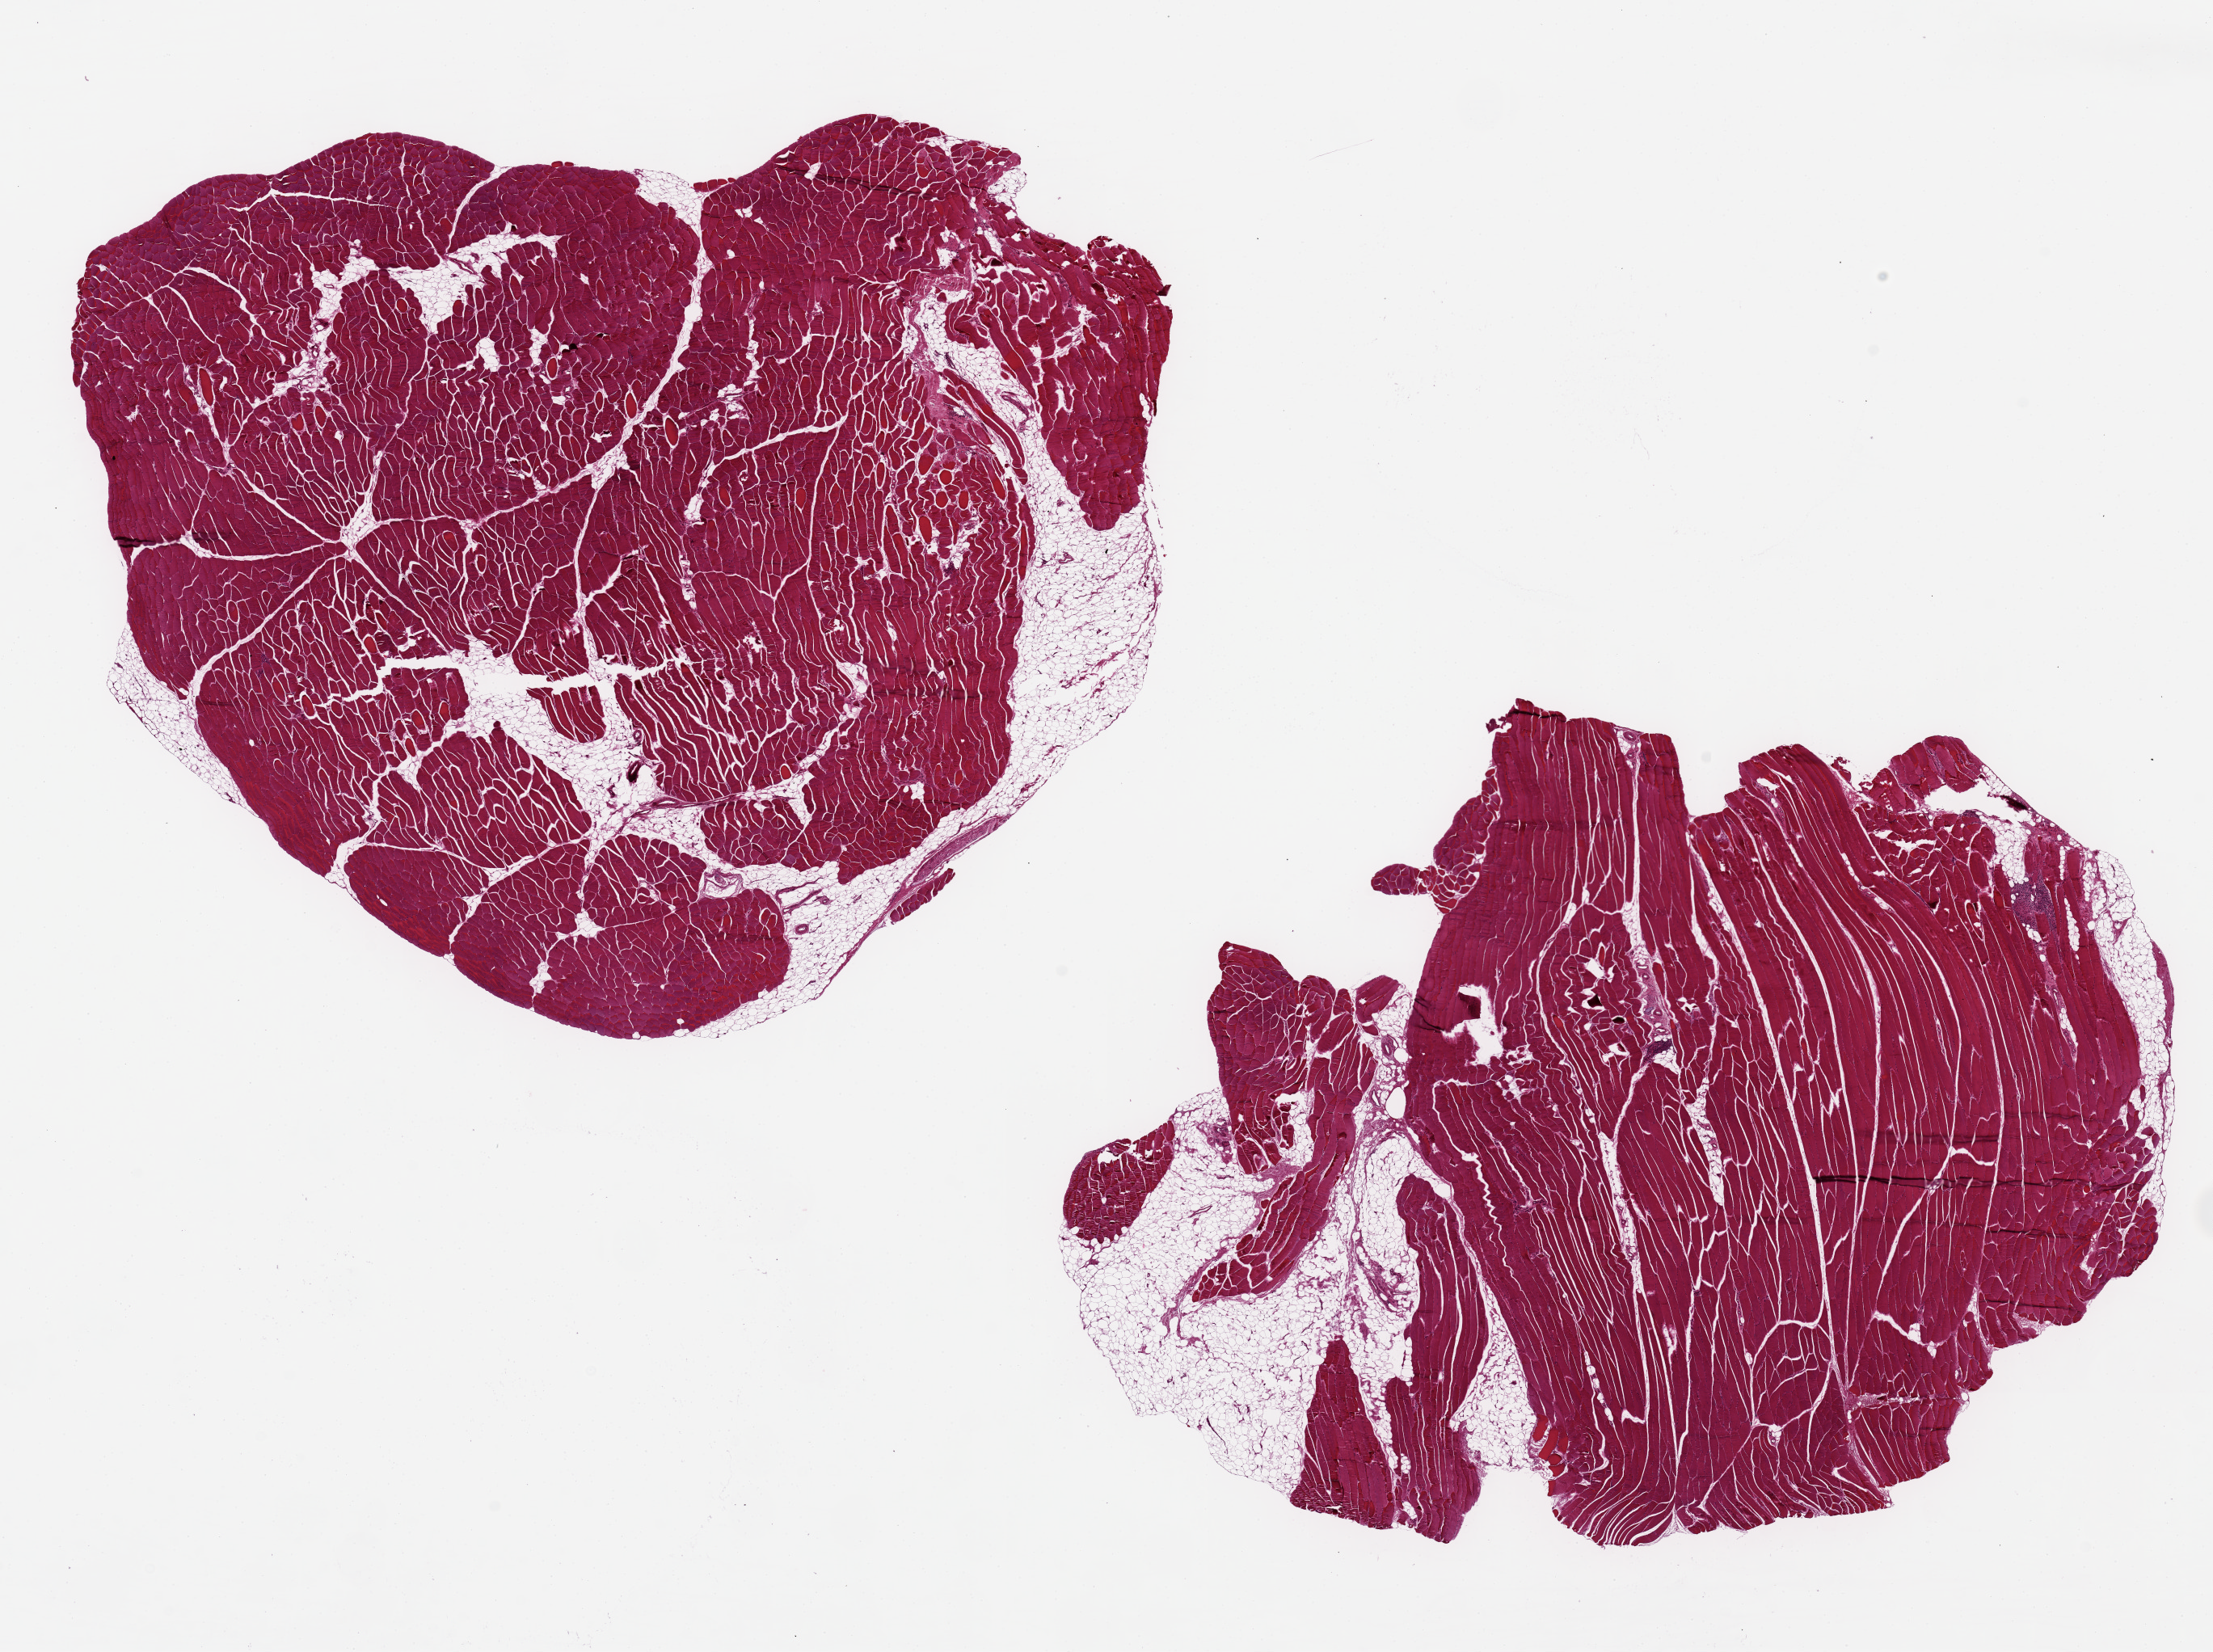
Whole-slide image, haematoxylin and eosin stain — shown as a low-resolution overview of the whole scanned area (about 21.7 x 16.2 mm), PAXgene-fixed paraffin-embedded (PFPE) section, sampled site (target tissue): skeletal muscle, donor tissue sample.
Review note (as recorded): 2 pieces, 10x10 & 11x8mm; minimal external adipose.